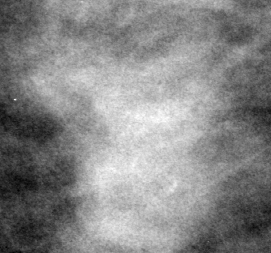
Region of interest cut from a scanned film mammogram (one marked finding); left breast; CC view.
- Marked abnormality: mass, shape lobulated, margins circumscribed / obscured; BI-RADS assessment category 4; pathology (as recorded): benign.